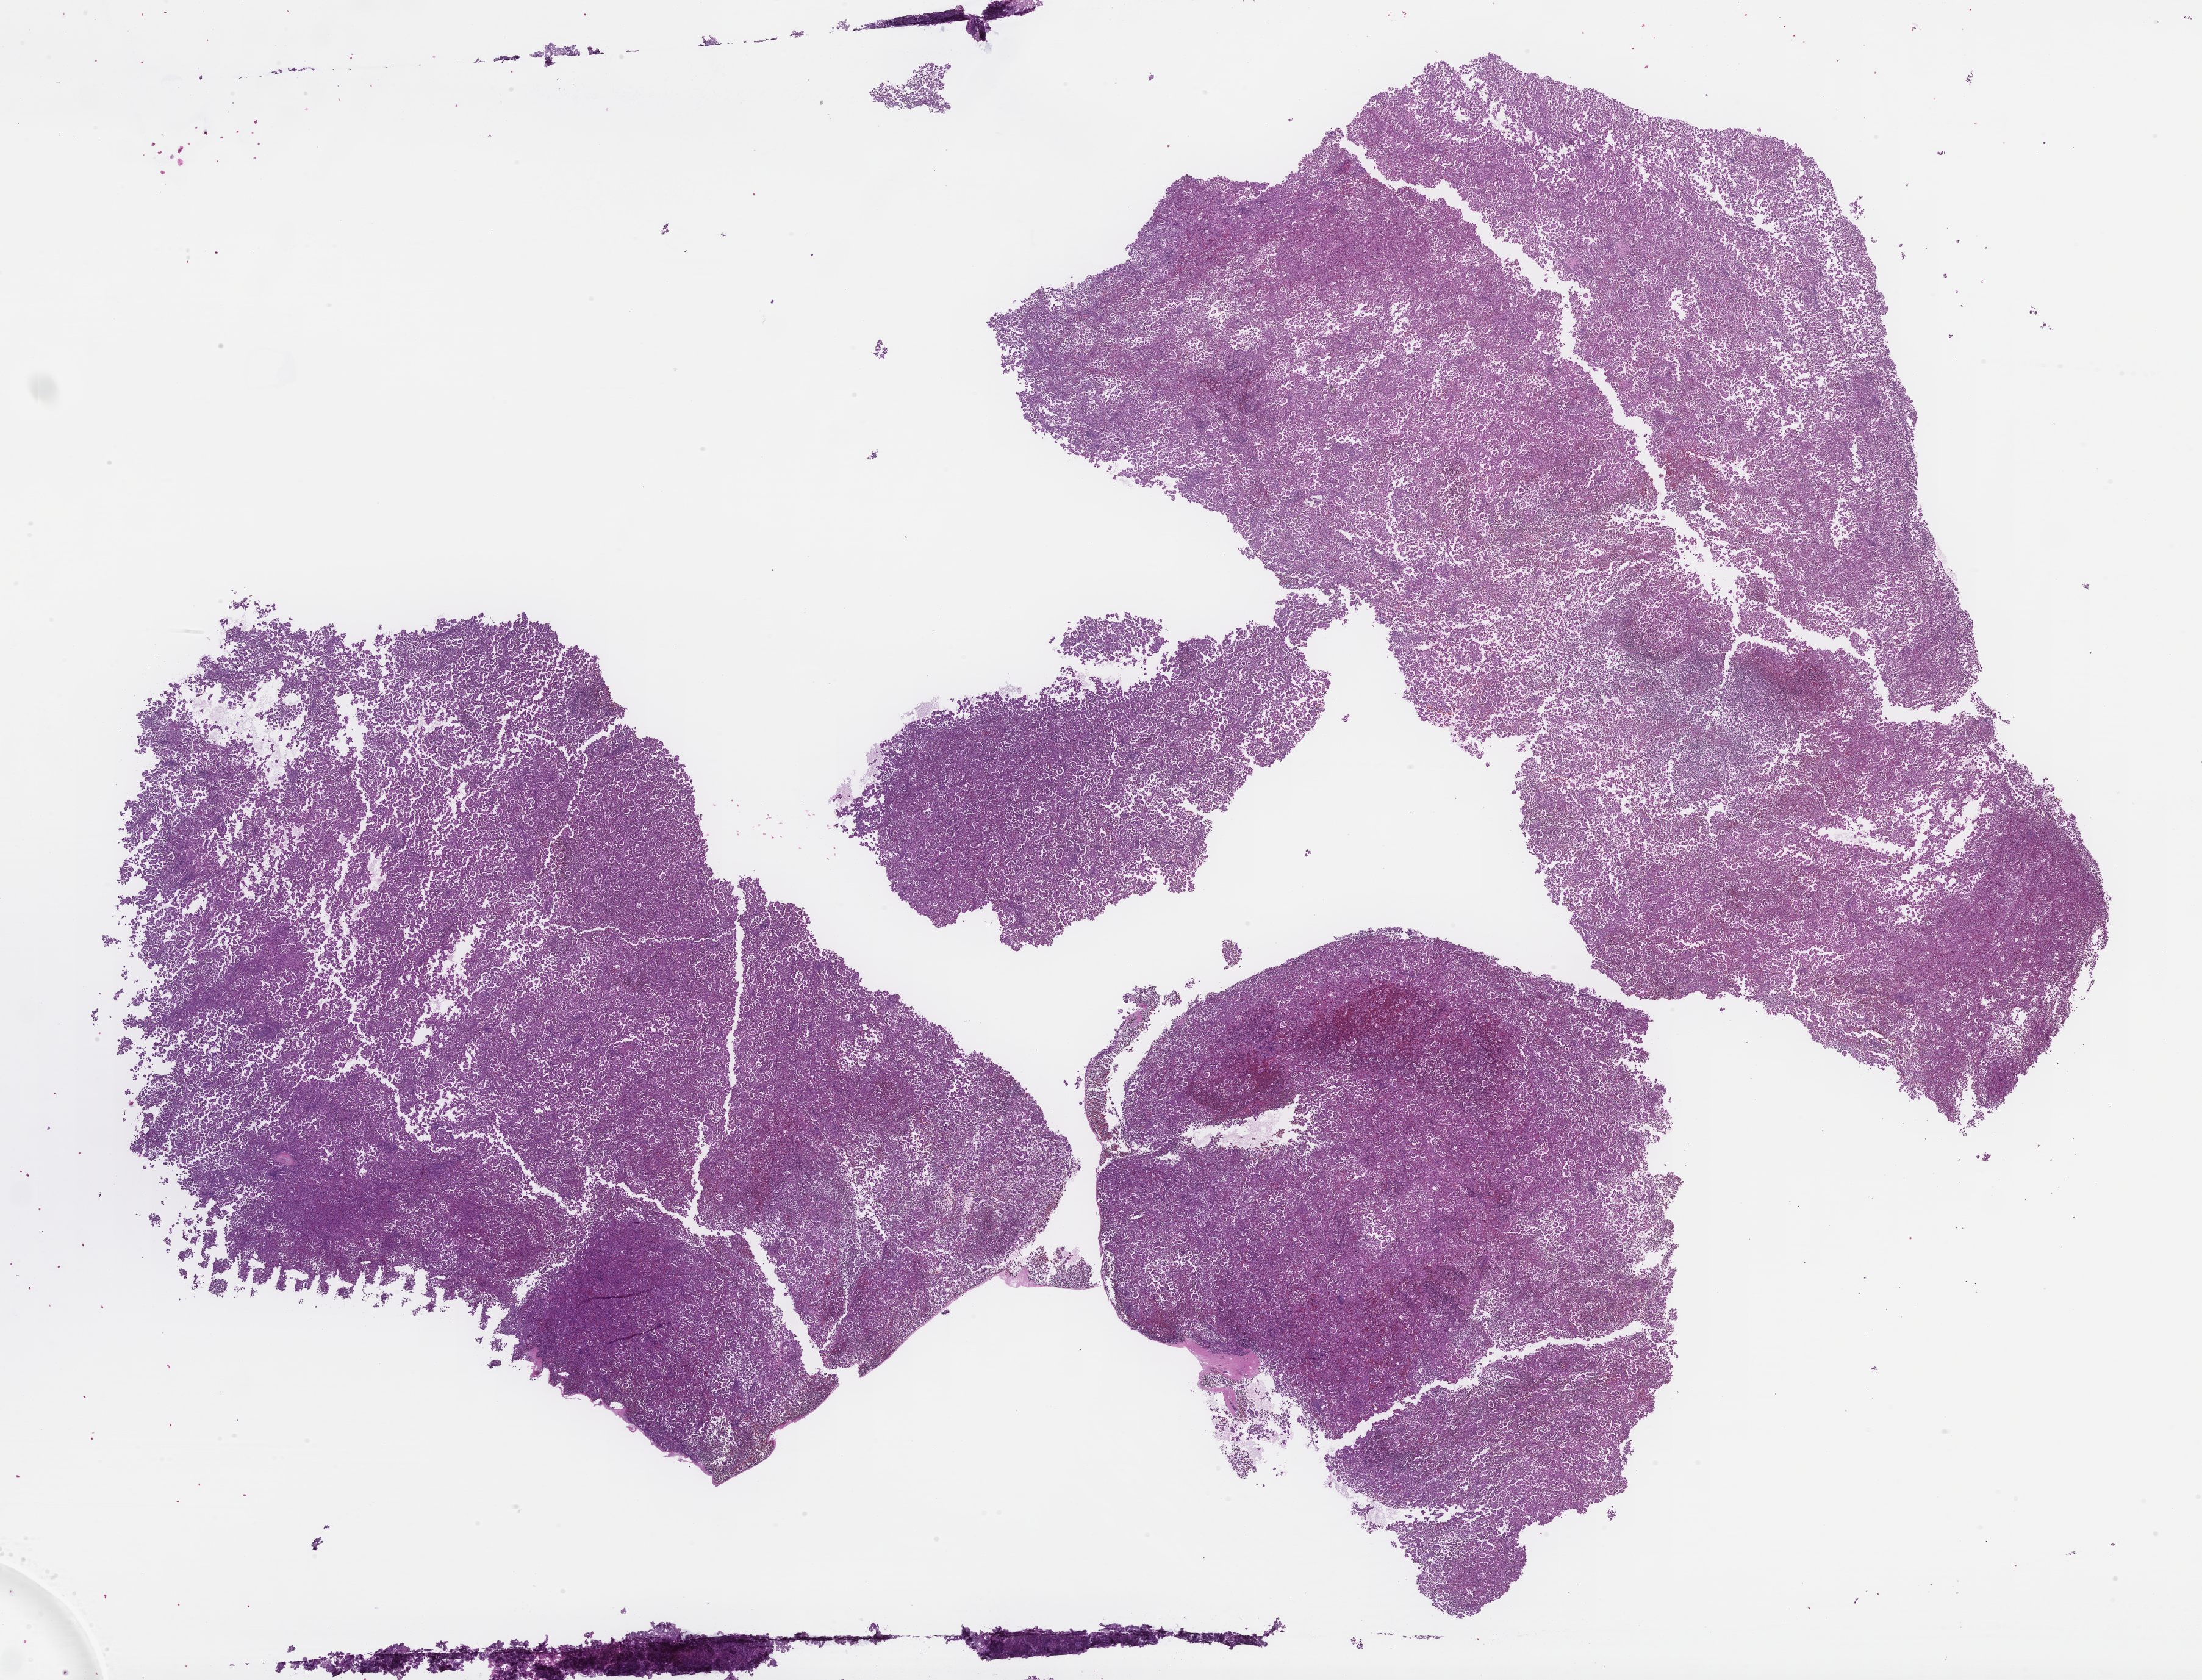
Haematoxylin and eosin whole-slide image, low-resolution overview of the scanned area, about 29.1 x 22.2 mm. Formalin-fixed paraffin-embedded section. Site: lung. Specimen time point: archival tissue. Patient: male.
This section: primary tumor. Diagnosis: Non-Small Cell Lung Carcinoma.